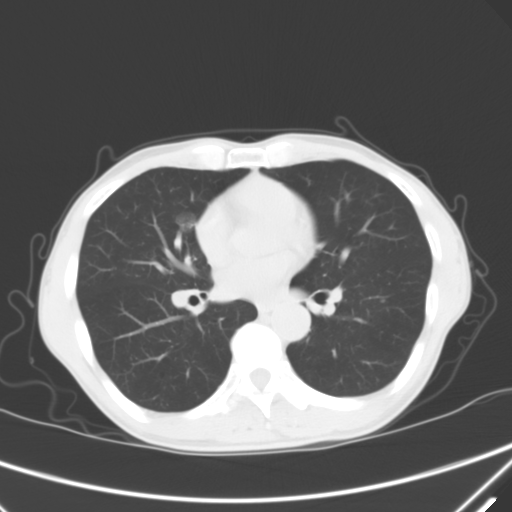
Chest CT, one axial slice; slice 33 of 68 in the series (ordered by position); lung window (W 1500 / L -600 HU); 512 × 512 image matrix, field of view 350 × 350 mm. Male patient, age 67 years. From the clinical record (not read from this slice): clinical TNM (as recorded): T1c N0 M0; histopathological grade: G1-2.
Outlined on this slice (rectangle marked by the reading radiologist):
- lung tumour (recorded histology: adenocarcinoma): box from (x=172, y=208) to (x=198, y=239) px